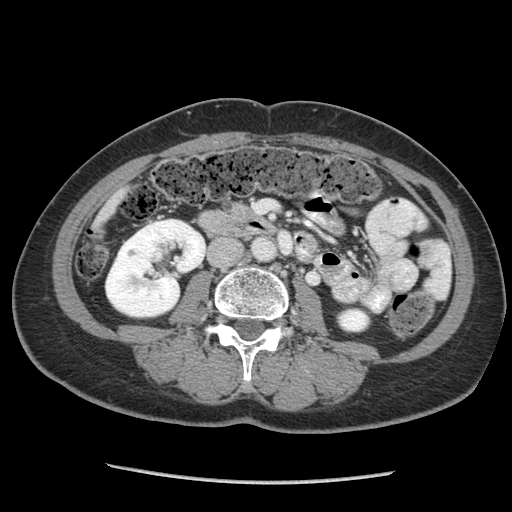
Contrast-enhanced abdominal CT (liver protocol), one axial slice; slice 14 of 105 in the series (ordered by position); reconstruction kernel STANDARD; 140 kVp; soft-tissue window (W 400 / L 40 HU); 2.5 mm slice thickness; 512 × 512 image matrix, field of view 340 × 340 mm. From the clinical record (not read from this slice): diagnosis: hepatocellular carcinoma (patient treated with transarterial chemoembolisation; whether this scan precedes or follows treatment is not stated here); TNM stage (as recorded): Stage-I; Child-Pugh class: A; tumour differentiation: moderately differentiated; tumour nodularity: uninodular.
Outlined on this slice (semi-automatic segmentation, software-assisted and operator-edited):
- liver parenchyma outside the tumour (the mass and vessels are separate outlines, so this box may not span the whole liver): box from (x=92, y=188) to (x=126, y=235) px